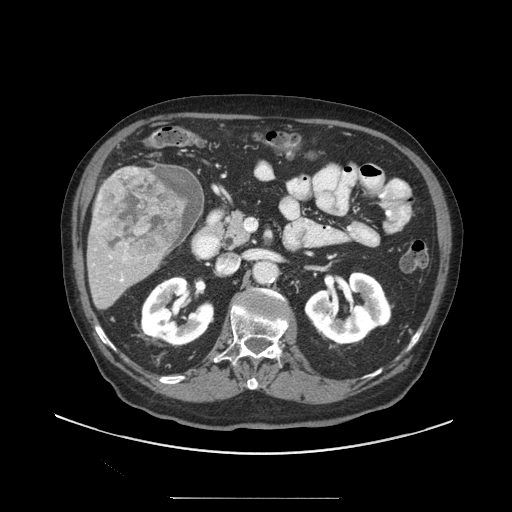
Contrast-enhanced abdominal CT (liver protocol), one axial slice. Position 43 of 97 along the scan axis. Soft-tissue window (W 400 / L 40 HU). 512 × 512 image matrix, field of view 450 × 450 mm. From the clinical record (not read from this slice): diagnosis: hepatocellular carcinoma (patient treated with transarterial chemoembolisation; whether this scan precedes or follows treatment is not stated here); TNM stage (as recorded): Stage-IIIC; Child-Pugh class: A; tumour nodularity: uninodular; tumour size: 9.2 cm.
Structures marked on this image (semi-automatically segmented with operator editing):
- liver parenchyma outside the tumour (the mass and vessels are separate outlines, so this box may not span the whole liver): bounding box [x1, y1, x2, y2] px = [86, 164, 202, 310]
- mass: [96, 167, 186, 258]
- liver vessels: [109, 256, 126, 282]